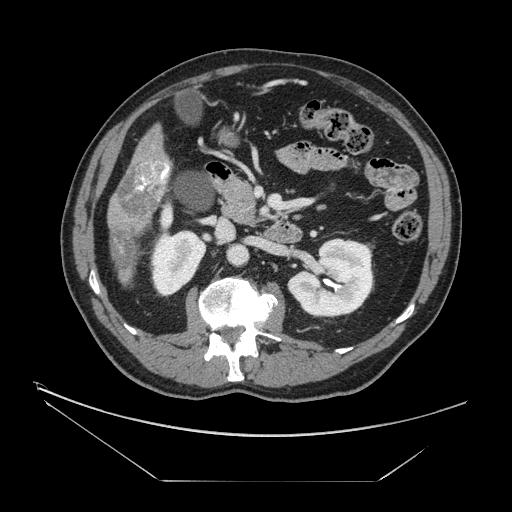
Contrast-enhanced abdominal CT, one axial slice. Slice 60 of 161 in the series (ordered by position). 120 kVp. Intravenous contrast given. Soft-tissue window (W 400 / L 40 HU). 2.5 mm slice thickness. 512 × 512 image matrix, field of view 440 × 440 mm. Male patient, age 65 years. From the clinical record (not read from this slice): diagnosis: colorectal cancer liver metastases, imaged before liver resection; multiple liver metastases: yes; largest metastasis: 4.2 cm; disease in both lobes: yes.
Annotated regions visible in this slice (expert manual segmentation):
- liver: bounding box (x1, y1, x2, y2) in pixels: (109, 128, 171, 283)
- portal vein (with intrahepatic branches): (137, 162, 169, 195)
- liver metastasis: (110, 230, 137, 272)
- liver metastasis: (117, 162, 171, 218)